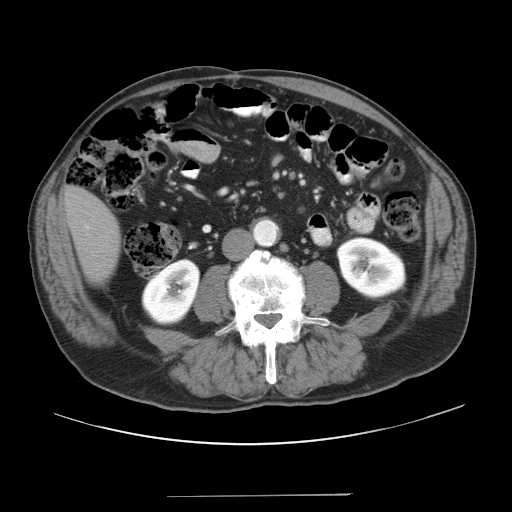
Contrast-enhanced abdominal CT, one axial slice. Position 2 of 41 along the scan axis. Reconstruction kernel STANDARD. 120 kVp. Intravenous contrast given. Soft-tissue window (W 400 / L 40 HU). 5 mm slice thickness. 512 × 512 image matrix, field of view 420 × 420 mm. Male patient, age 75 years. From the clinical record (not read from this slice): diagnosis: colorectal cancer liver metastases, imaged before liver resection; multiple liver metastases: no; largest metastasis: 5.2 cm; disease in both lobes: no.
Outlined on this slice (expert manual segmentation):
- liver: bounding box <65,188,120,281> (left, top, right, bottom; pixels)
- planned liver remnant (the part of the liver to remain after resection): <65,188,120,281>
- portal vein (with intrahepatic branches): <85,225,90,229>